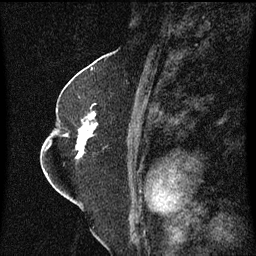
Breast MRI (dynamic contrast-enhanced), one sagittal slice; position 35 of 60 along the scan axis; dynamic contrast-enhanced series, image 2 of 3 at this slice position (ordered by acquisition); 1.5 T; TE 4.2 ms, TR 8.4 ms; 2 mm slice thickness; 256 × 256 image matrix, field of view 200 × 200 mm. Patient: female, 52 years. Case-level facts recorded for this patient, not image findings: setting: breast cancer imaged before/during neoadjuvant chemotherapy; receptor status: HR-positive, HER2-negative.
Annotated regions visible in this slice (semi-automatically segmented with operator editing):
- analysis volume of interest (the breast-tissue region the enhancement analysis was run in; not a lesion): box from (x=64, y=110) to (x=99, y=163) px
- tumour enhancement mask (voxels above the 70 % enhancement threshold inside the analysis volume of interest): (x=77, y=112)–(x=98, y=159)